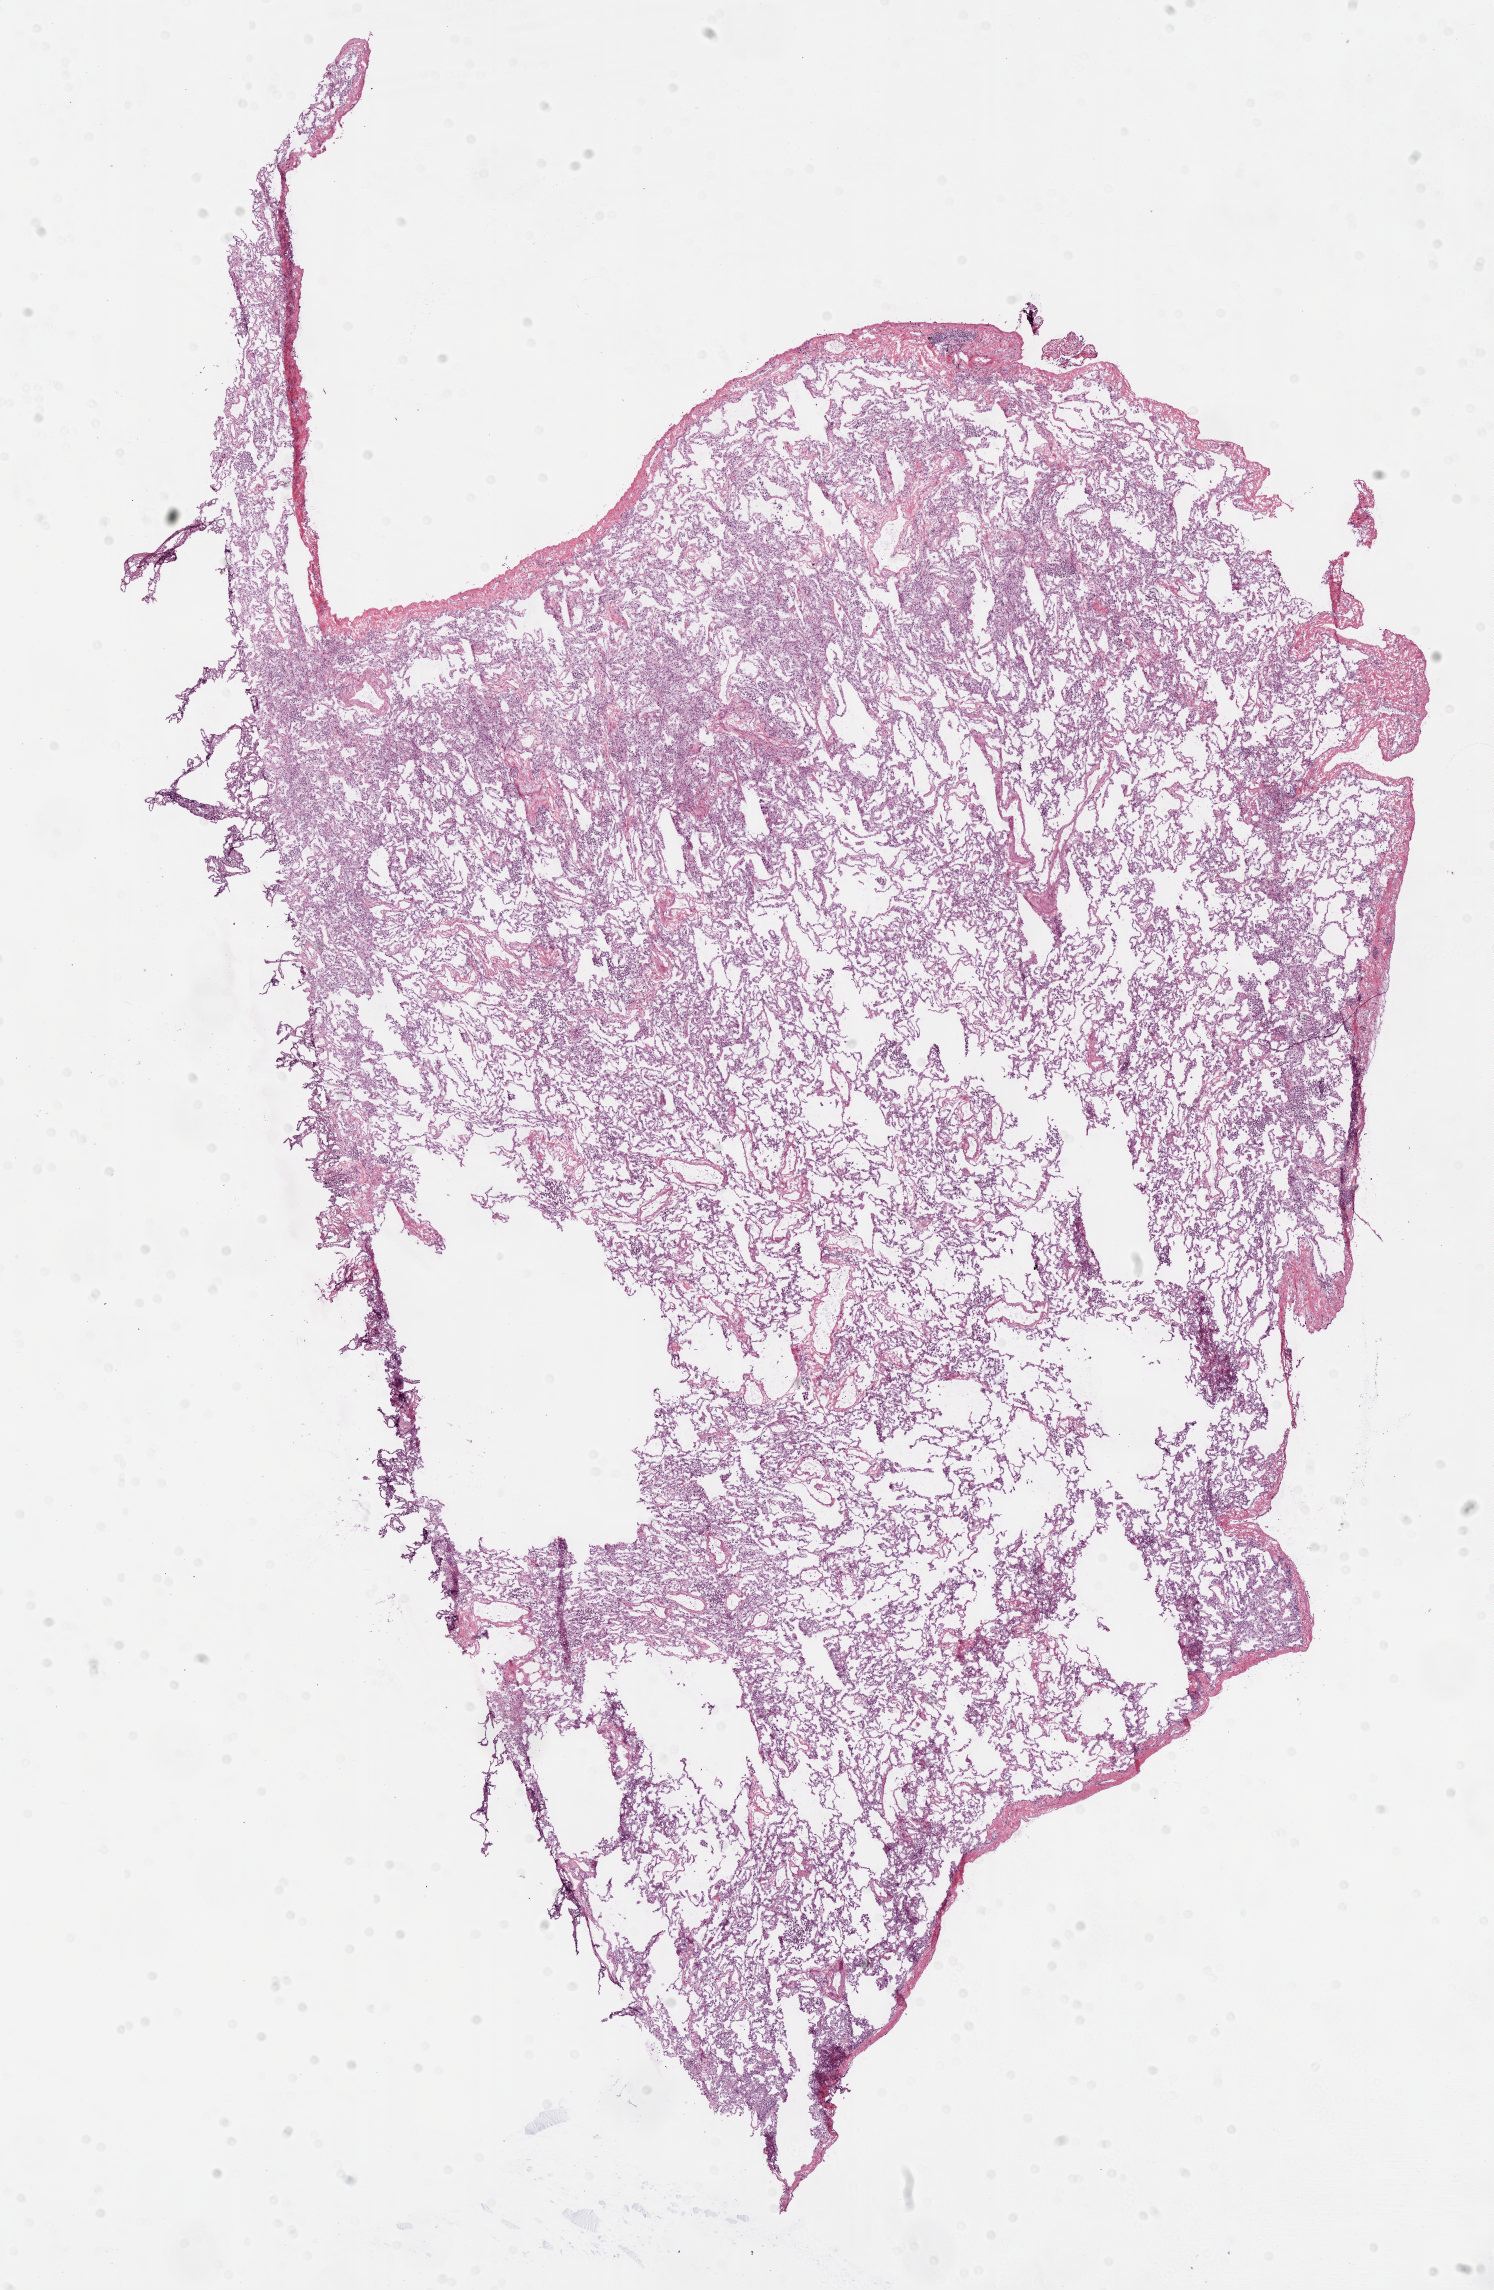
Digitized Hematoxylin and eosin (H&E) stained tissue section (whole slide) — whole scanned area (about 12.0 x 18.5 mm, acquisition: 20x scan) shown as a low-resolution overview, frozen section from the top of the tissue portion, lung, solid tissue normal (non-tumour tissue) sample. Patient: female, age at initial diagnosis 63 years.
* this section: solid tissue normal sample (biorepository sample class)
* patient diagnosis: Adenocarcinoma, NOS (lower lobe, lung)